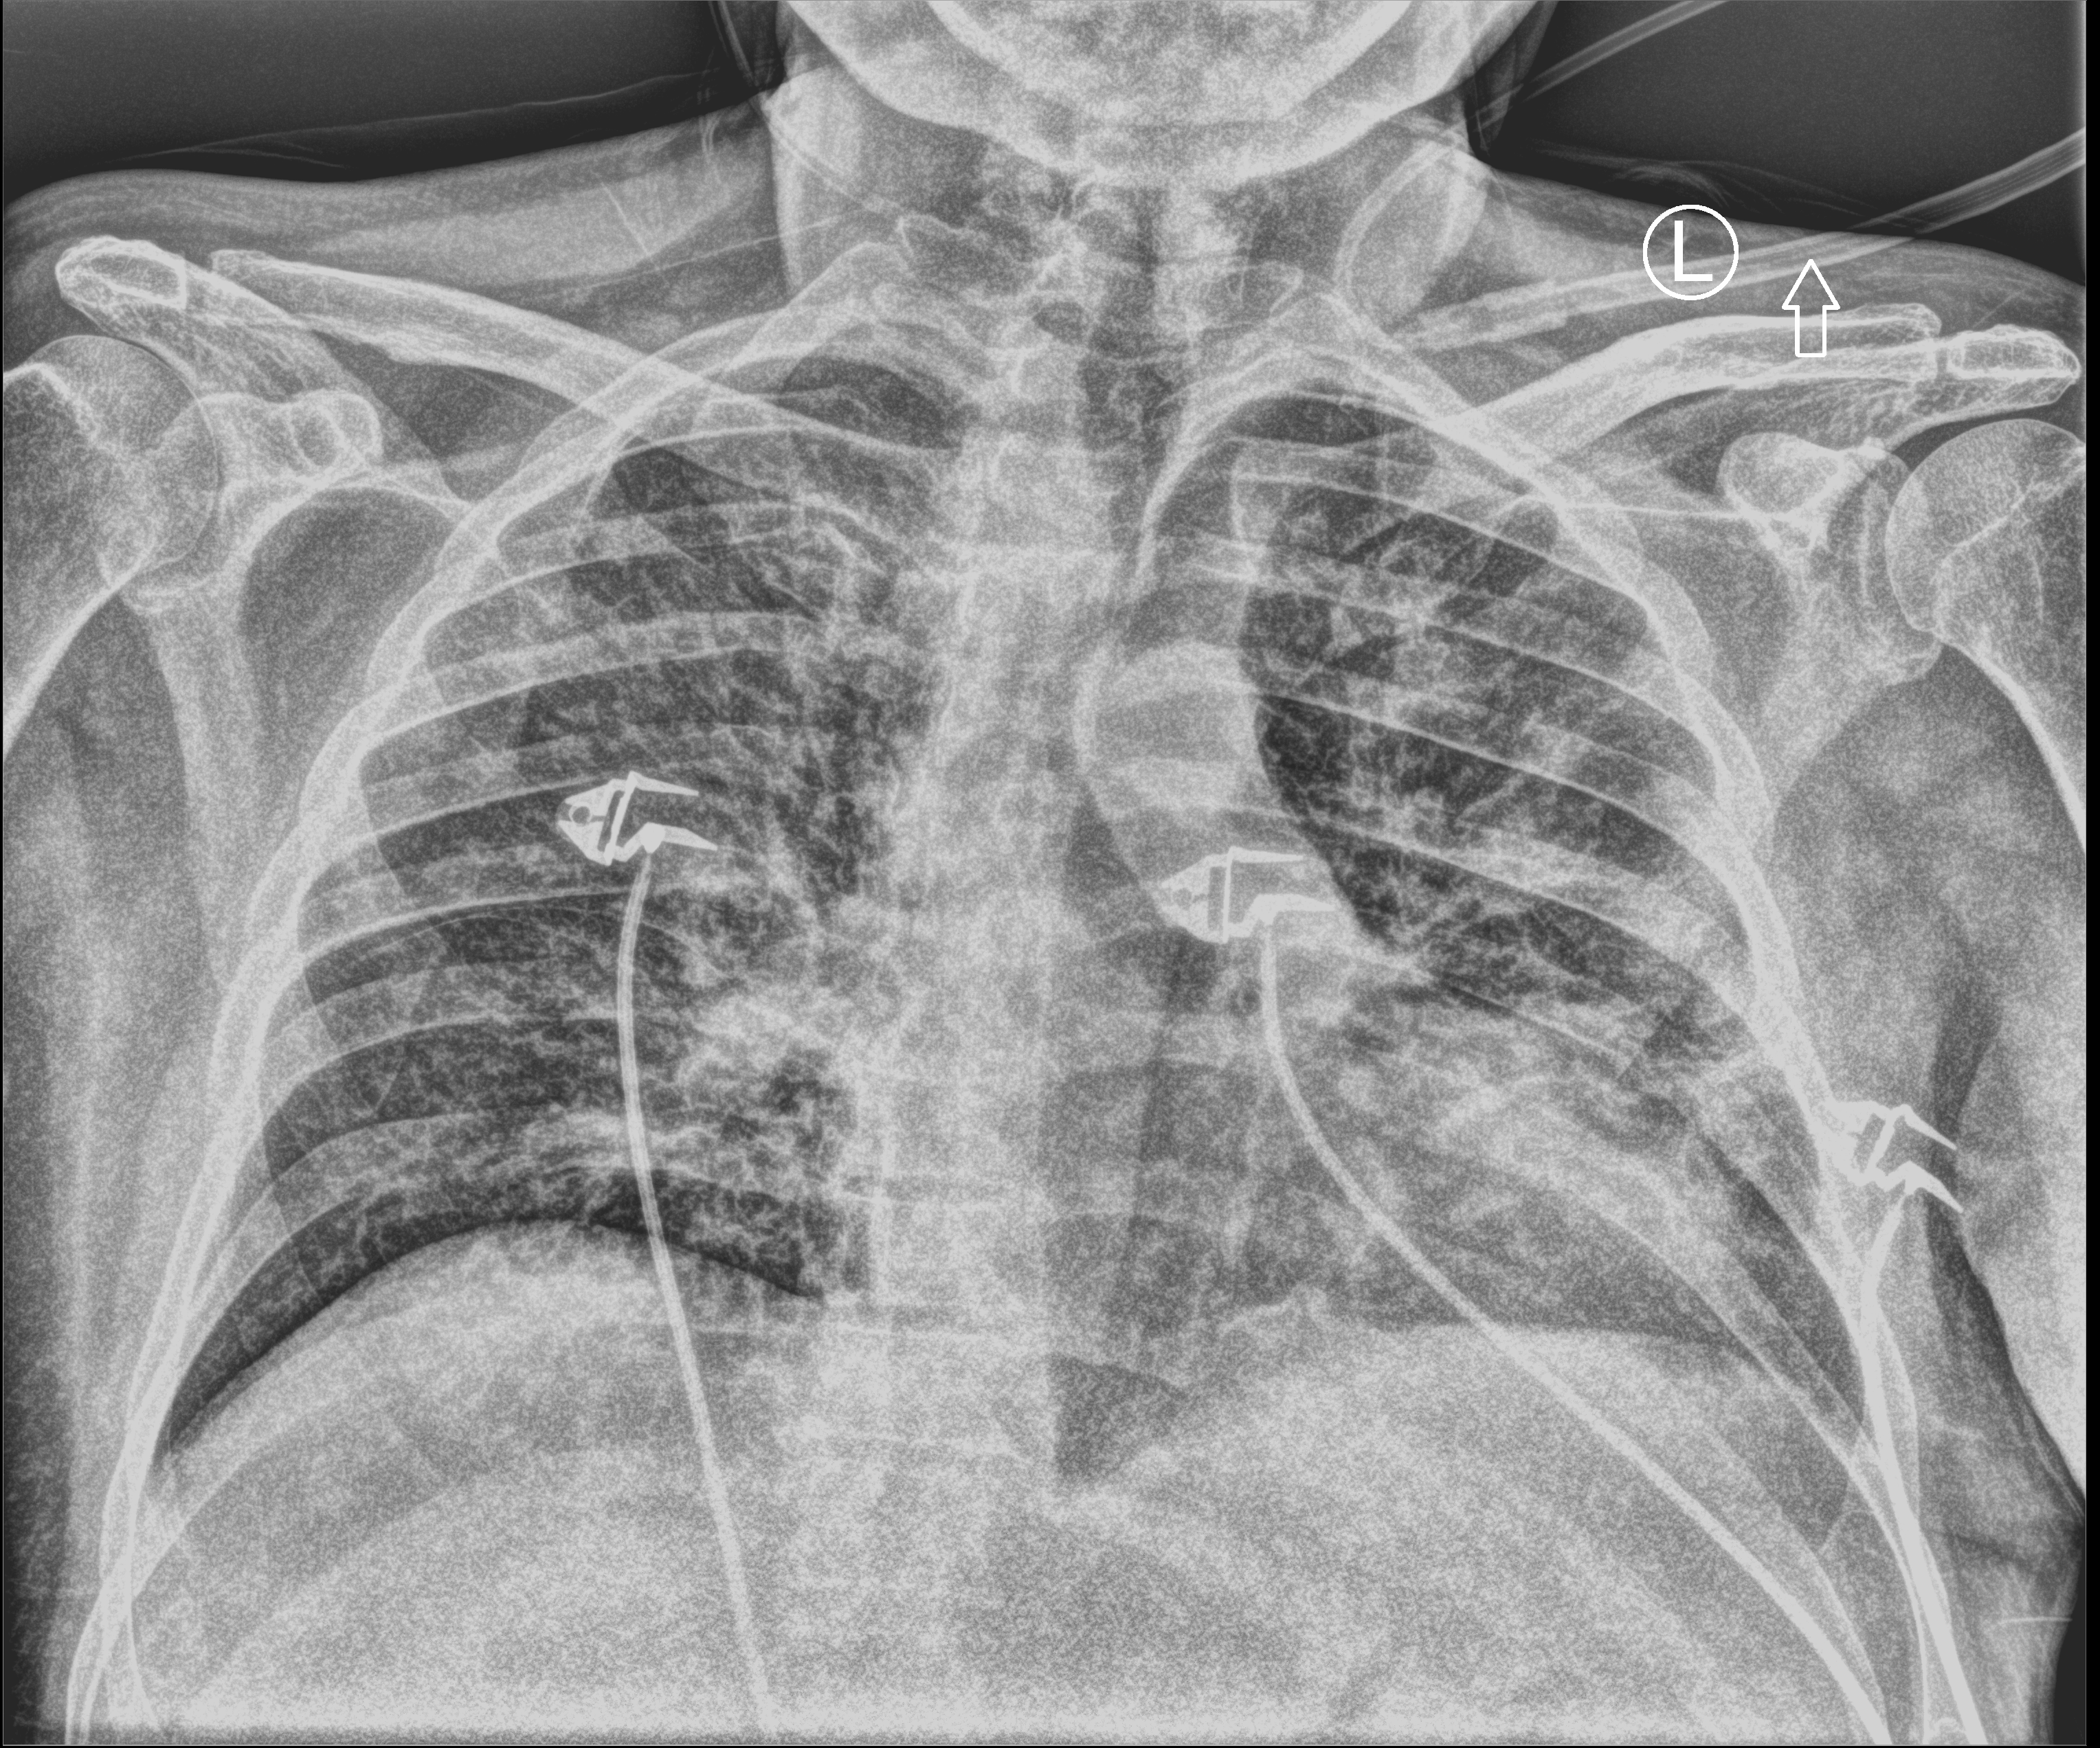
Portable chest radiograph. Male patient hospitalised with COVID-19, age 60–74 years.
Admission-level facts for this patient (not findings on this image; timing relative to this image not recorded): admitted to intensive care during this hospital stay: yes.